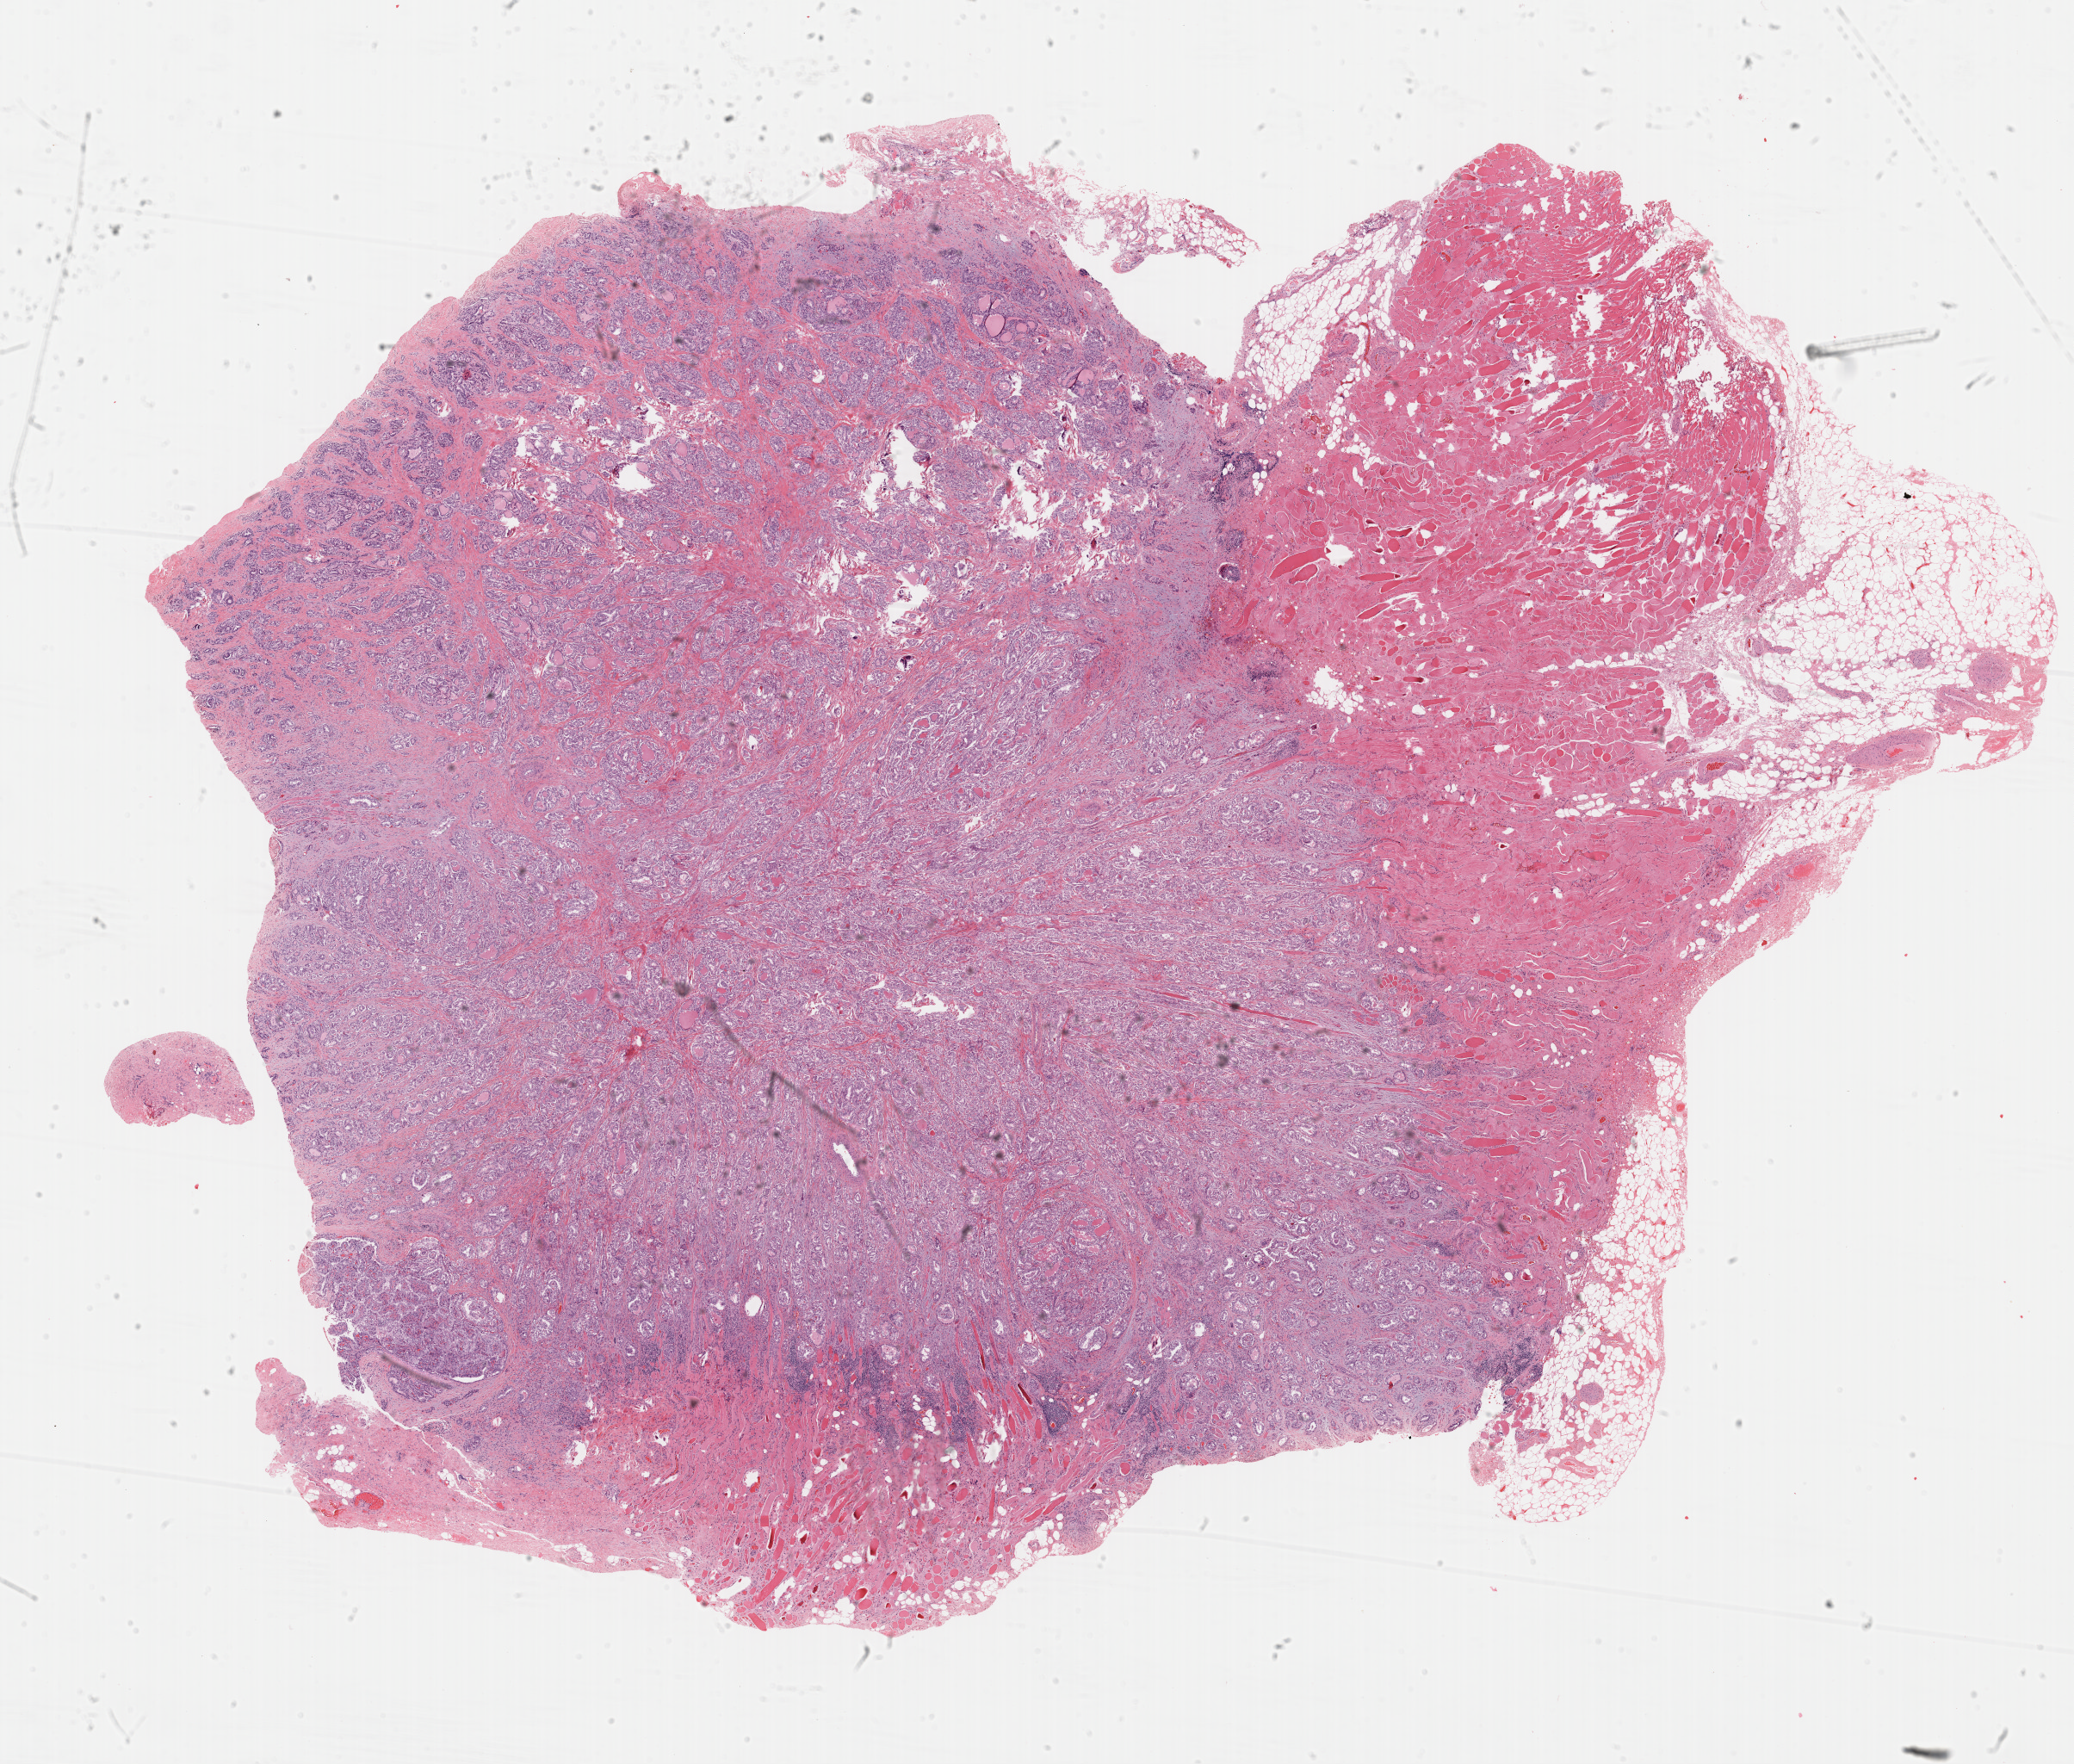
Digitized H&E-stained tissue section (whole slide) — low-resolution overview of the scanned area, about 19.0 x 16.2 mm (slide scanned at 40x), formalin-fixed paraffin-embedded (FFPE) diagnostic section, primary tumour sample from the thyroid. Female patient; age at initial diagnosis 78 years.
Histologic diagnosis: Papillary adenocarcinoma, NOS (thyroid gland).